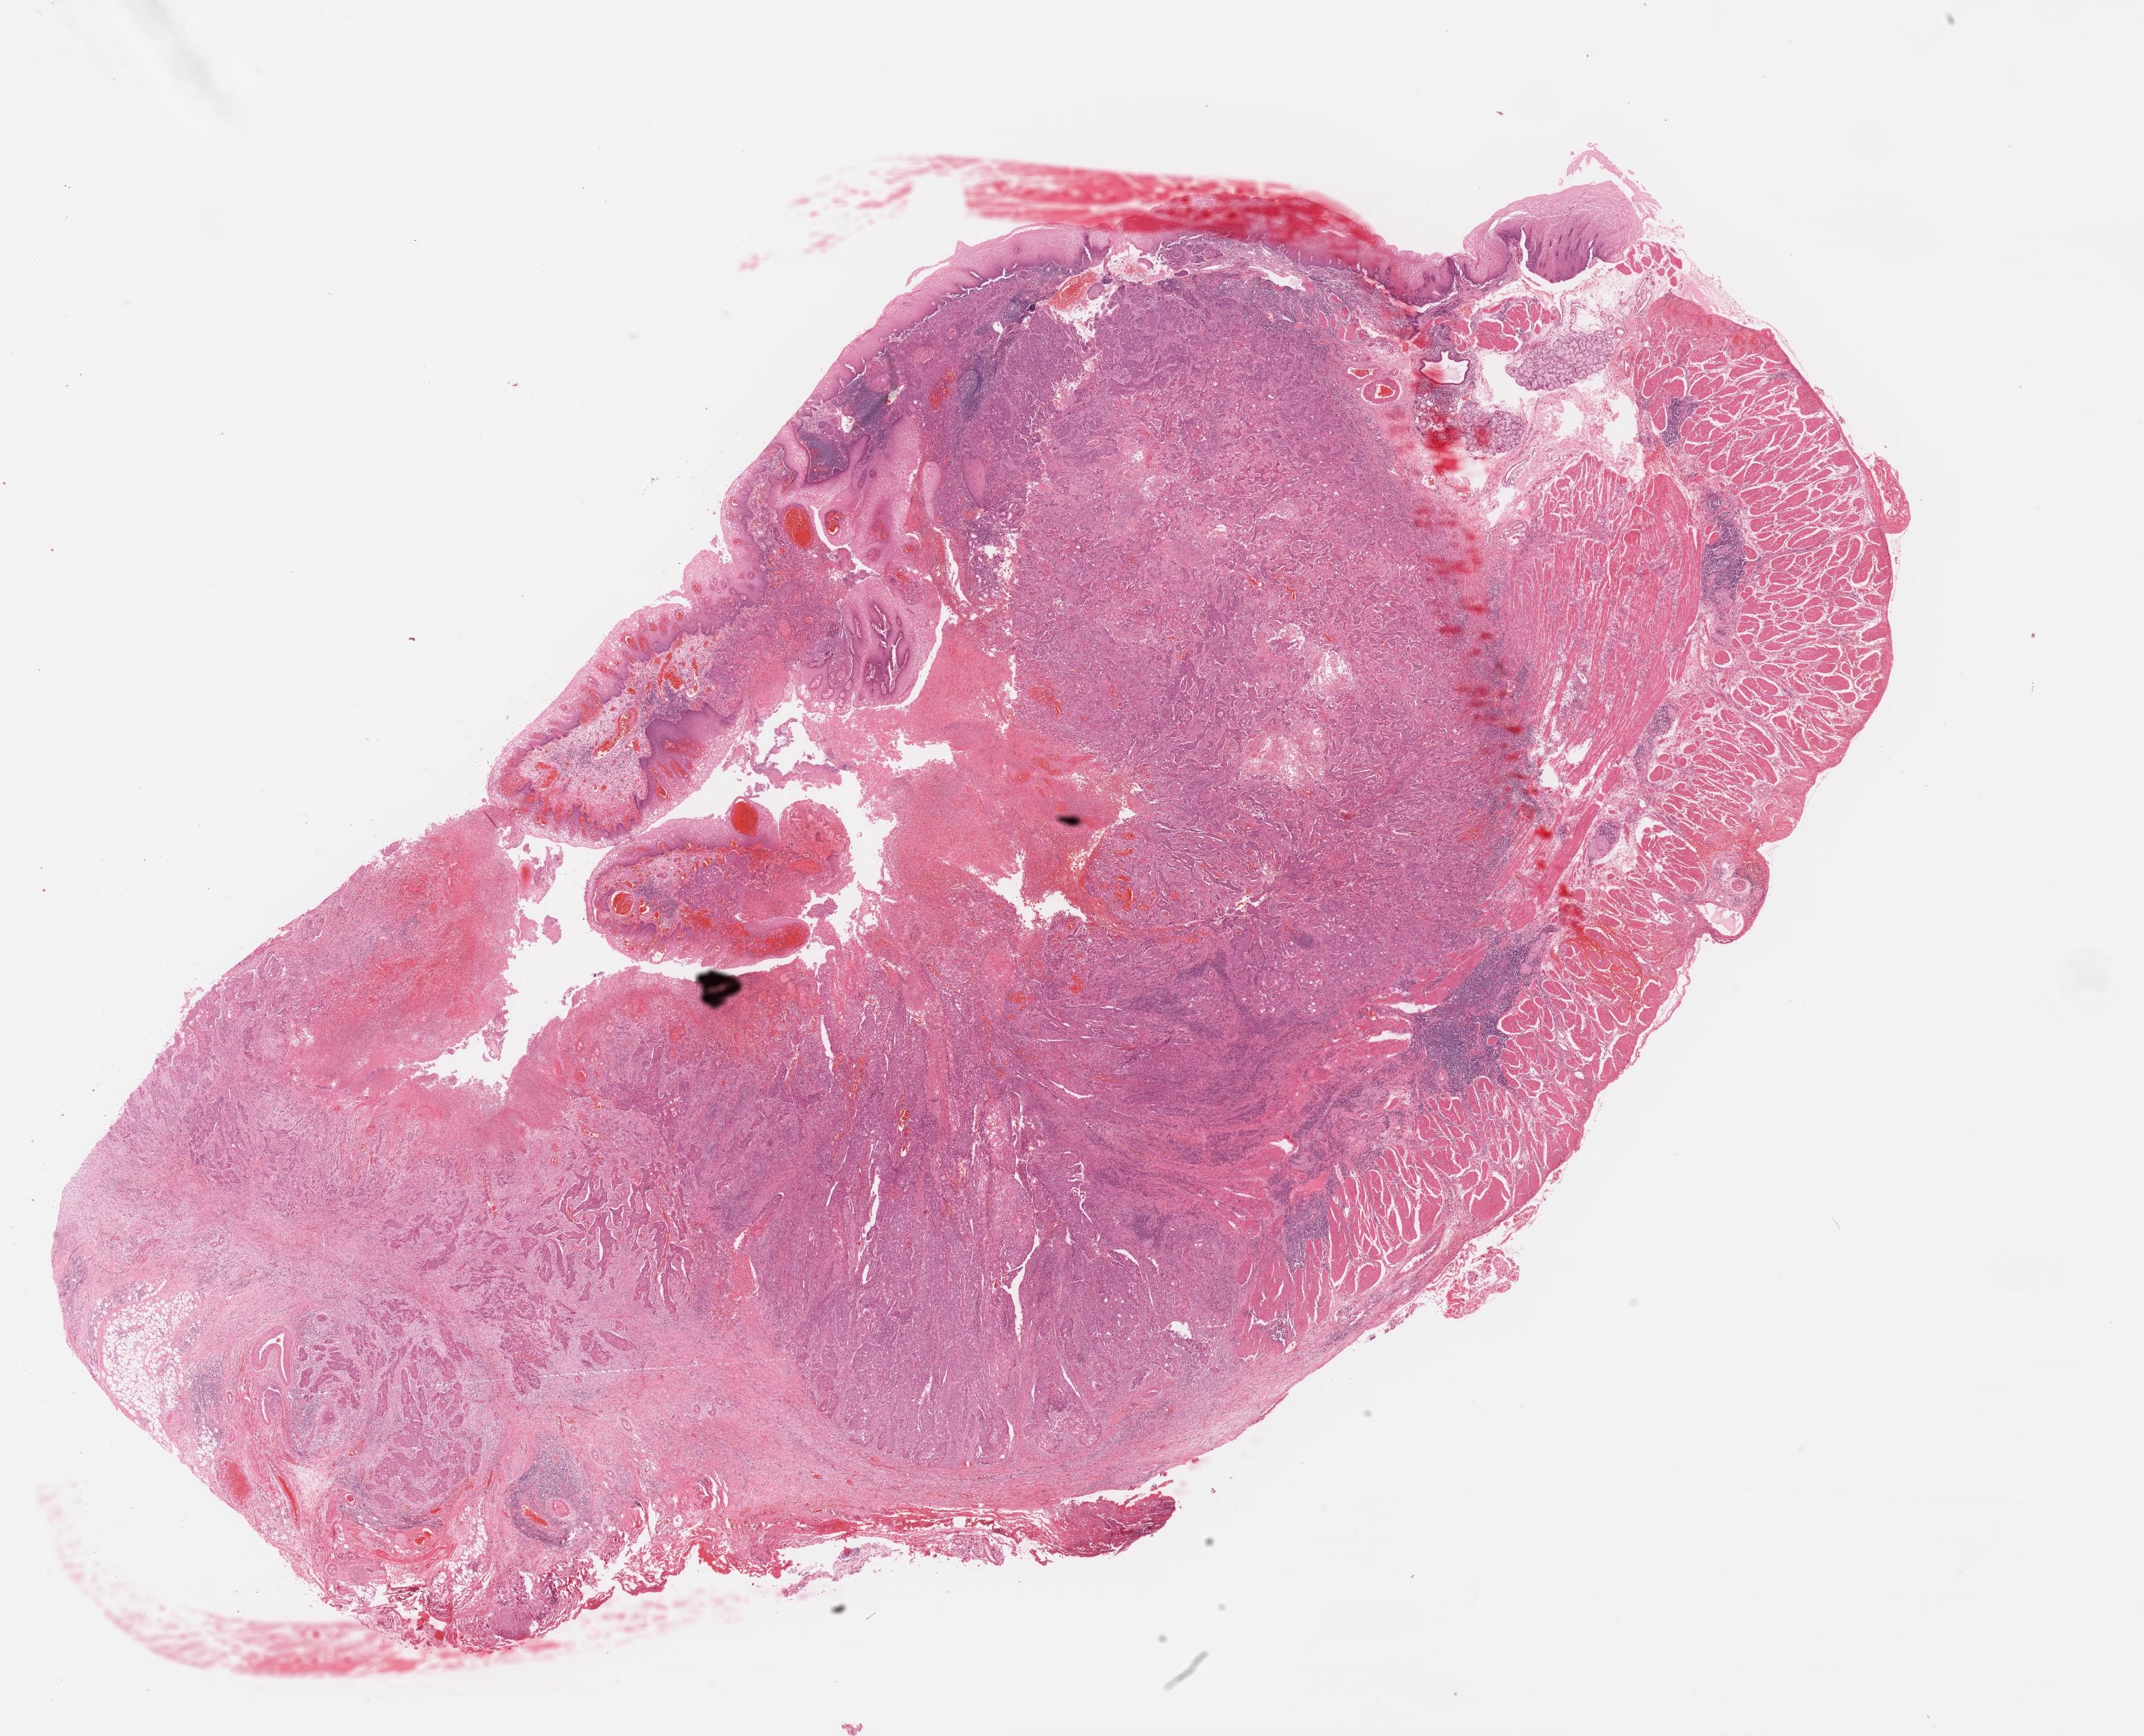
H&E whole-slide image, a low-resolution overview of the entire scanned area, about 24.8 x 20.1 mm (from a 40x scan); formalin-fixed paraffin-embedded (FFPE) diagnostic section; sample: primary tumour, esophagus. Male, age 58 years at initial diagnosis. Histologic grade: G2 (moderately differentiated).
TNM: T3 N1 M0. Histologic diagnosis: Squamous cell carcinoma, NOS (lower third of esophagus). AJCC pathologic stage: IIIA. Lymph nodes positive (case pathology): 1 of 1 examined.